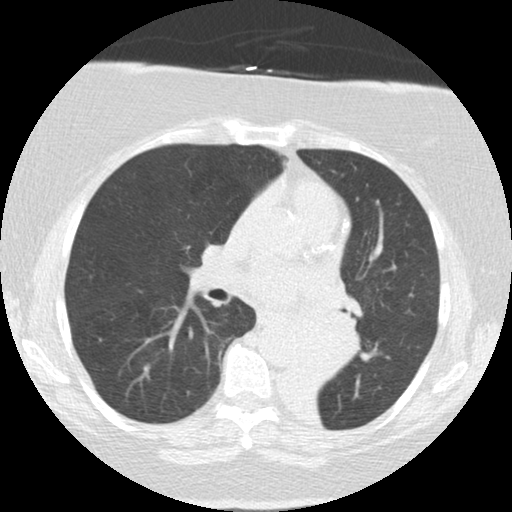
Chest CT (low-dose screening protocol), one axial image. First (baseline) screen. Lung window (W 1500 / L -600 HU). 2.5 mm slice thickness. Standard (soft-tissue) reconstruction kernel (STANDARD). 120 kVp. Female participant, aged 71 years at enrolment. Former smoker at enrolment.
- Expert-annotated lung lesion, bounding box [x1, y1, x2, y2] px = [287, 307, 364, 383].
- Screening reader's record for this exam (one nodule recorded; not confirmed to be the boxed lesion): non-calcified nodule or mass ≥4 mm, right middle lobe, 5 × 5 mm, smooth margins, soft tissue attenuation.
- Note: the box lies in the patient's left hemithorax on this image, whereas the reader's record names the right lung; they may be different findings.
- Official screen result: positive, change unspecified: nodule(s) >= 4 mm or enlarging nodule(s), mass(es), or other non-specific abnormalities suspicious for lung cancer.
- Later outcome: lung cancer diagnosed 46 days after this screen — large cell carcinoma, NOS, left lower lobe, mediastinum, other location, poorly differentiated (G3), stage IV (AJCC 6th edition), 50 mm at pathology.